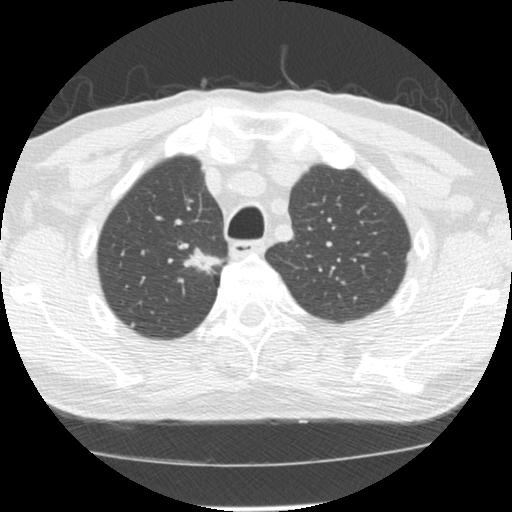
Low-dose screening chest CT, one axial slice; slice 109 of 139 in the series (ordered by position); reconstruction kernel STANDARD; lung window (W 1500 / L -600 HU); 2.5 mm slice thickness; 512 × 512 image matrix.
Annotated regions visible in this slice (outlined manually by an expert reader):
- lesion 1 (tumor, upper lobe of right lung): bounding box <183,247,225,275> (left, top, right, bottom; pixels)